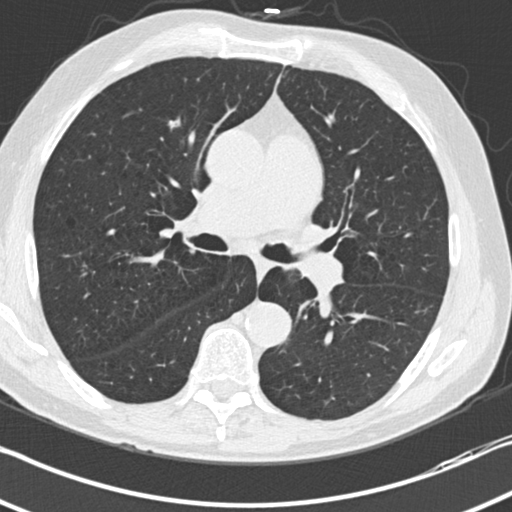
Chest CT (low-dose screening protocol), one axial image, third annual screen, lung window (W 1500 / L -600 HU). Male, age 70 years at enrolment. Current smoker at enrolment.
• Expert reader's lesion annotation, bounding box [x1, y1, x2, y2] px = [154, 110, 192, 143].
• The exam's reader record, not a measurement of the box and not confirmed to be the same lesion: non-calcified nodule or mass ≥4 mm, right middle lobe, 9 × 8 mm, smooth margins, soft tissue attenuation, pre-existing on the prior screen: no.
• Official screen result: positive, other.
• Later outcome: lung cancer diagnosed 53 days after this screen — squamous cell carcinoma, NOS, right upper lobe, moderately differentiated (G2), stage IA (AJCC 6th edition), 10 mm at pathology.